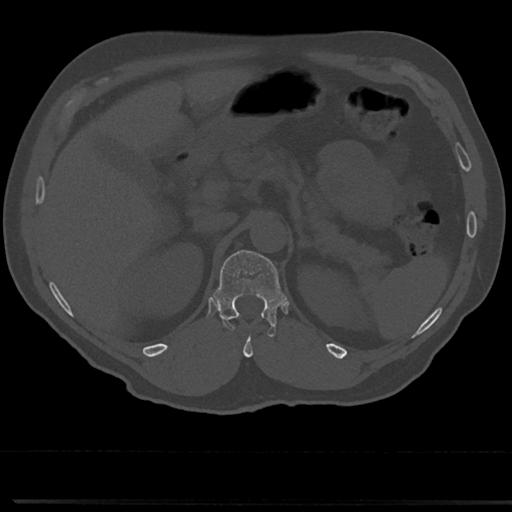
CT including the spine, one axial slice; position 160 of 817 along the scan axis; reconstruction kernel Br40s/3; 120 kVp; bone window (W 1800 / L 400 HU); 0.5 mm slice thickness; 512 × 512 image matrix, field of view 355 × 355 mm. Male patient, age 61 years. Case-level facts recorded for this patient, not image findings: primary cancer: prostate.
Outlined on this slice (semi-automatically segmented with operator editing):
- T12 vertebra: bounding box (x1, y1, x2, y2) in pixels: (217, 249, 282, 334)